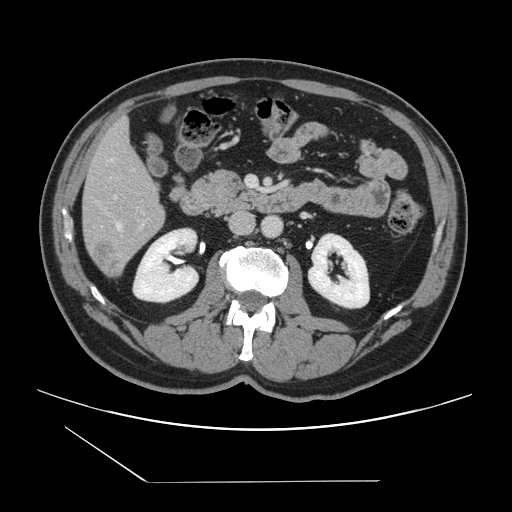
Contrast-enhanced abdominal CT, one axial slice; slice 50 of 157 in the series (ordered by position); 120 kVp; intravenous contrast given; soft-tissue window (W 400 / L 40 HU); 2.5 mm slice thickness; 512 × 512 image matrix. Male patient, age 61 years. From the clinical record (not read from this slice): diagnosis: colorectal cancer liver metastases, imaged before liver resection; multiple liver metastases: yes; largest metastasis: 5.5 cm.
Structures marked on this image (outlined manually by an expert reader):
- hepatic veins: bounding box (x1, y1, x2, y2) in pixels: (111, 159, 122, 229)
- liver: (83, 121, 164, 276)
- planned liver remnant (the part of the liver to remain after resection): (83, 121, 162, 218)
- portal vein (with intrahepatic branches): (115, 196, 144, 225)
- liver metastasis: (94, 240, 121, 275)